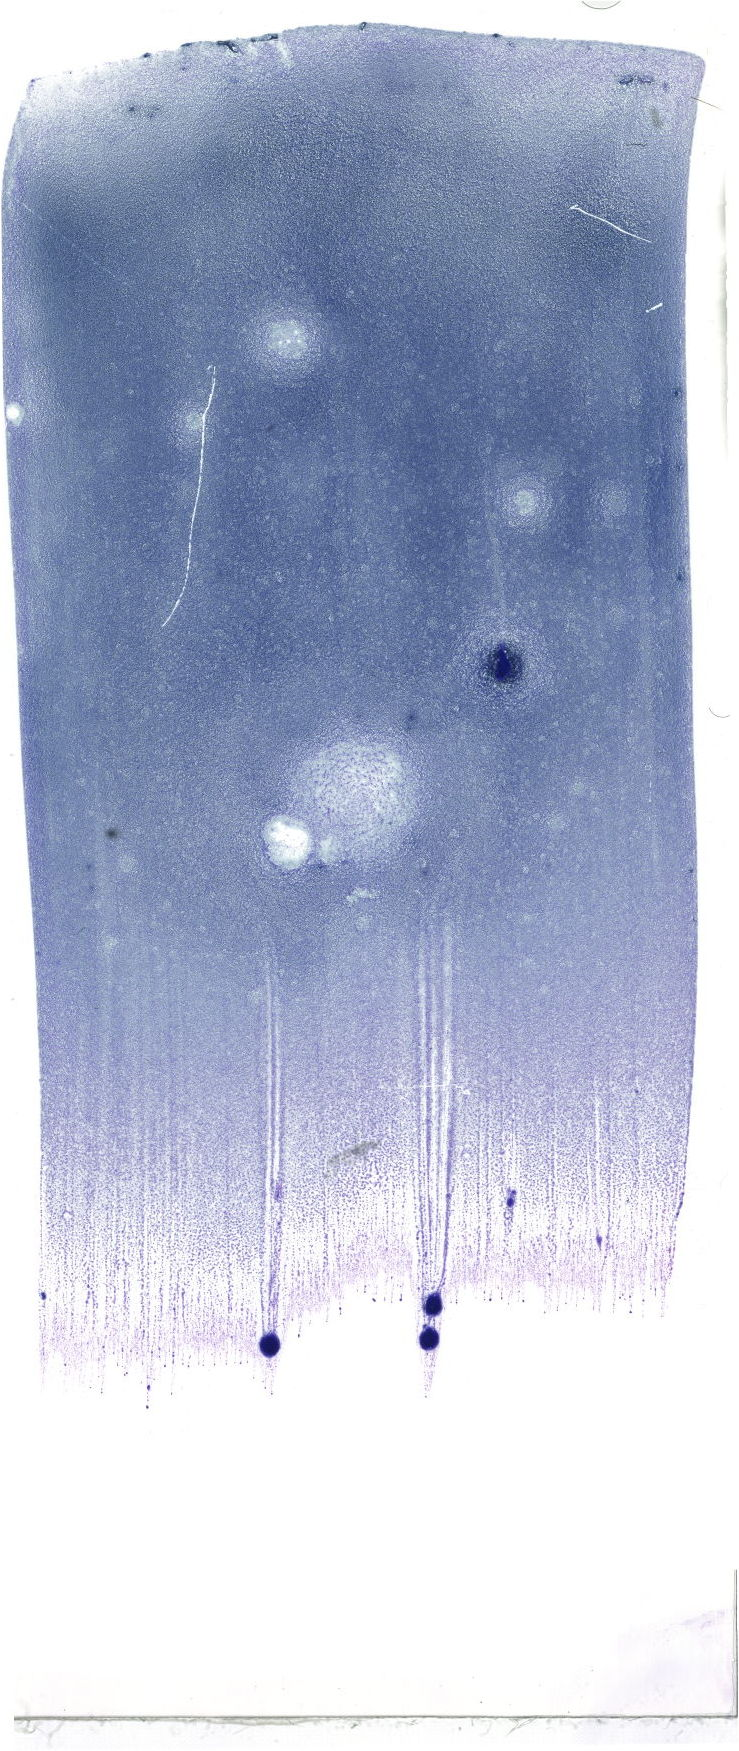
Bone marrow aspirate smear, May-Grünwald-Giemsa (MGG) stain, whole-slide image, a low-resolution overview of the entire scanned area, about 20.9 x 49.6 mm. Patient sex: male.
* diagnosis: Chronic Phase Chronic Myeloid Leukemia, BCR-ABL1 Positive